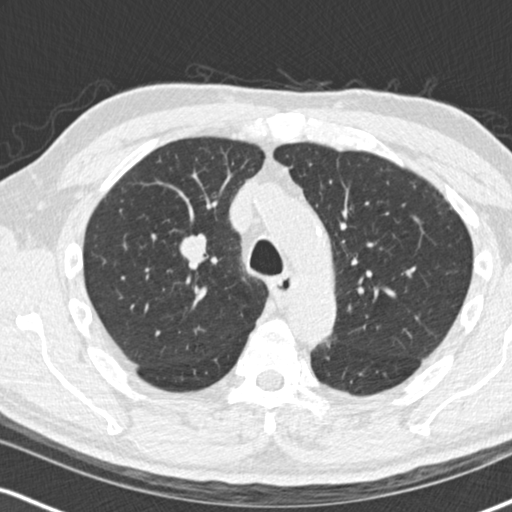
Low-dose screening chest CT, one axial slice; position 110 of 170 along the scan axis; 120 kVp; lung window (W 1500 / L -600 HU); 512 × 512 image matrix, field of view 320 × 320 mm.
Structures marked on this image (outlined manually by an expert reader):
- lesion 1 (tumor, upper lobe of right lung): bounding box [x1, y1, x2, y2] px = [180, 233, 207, 262]